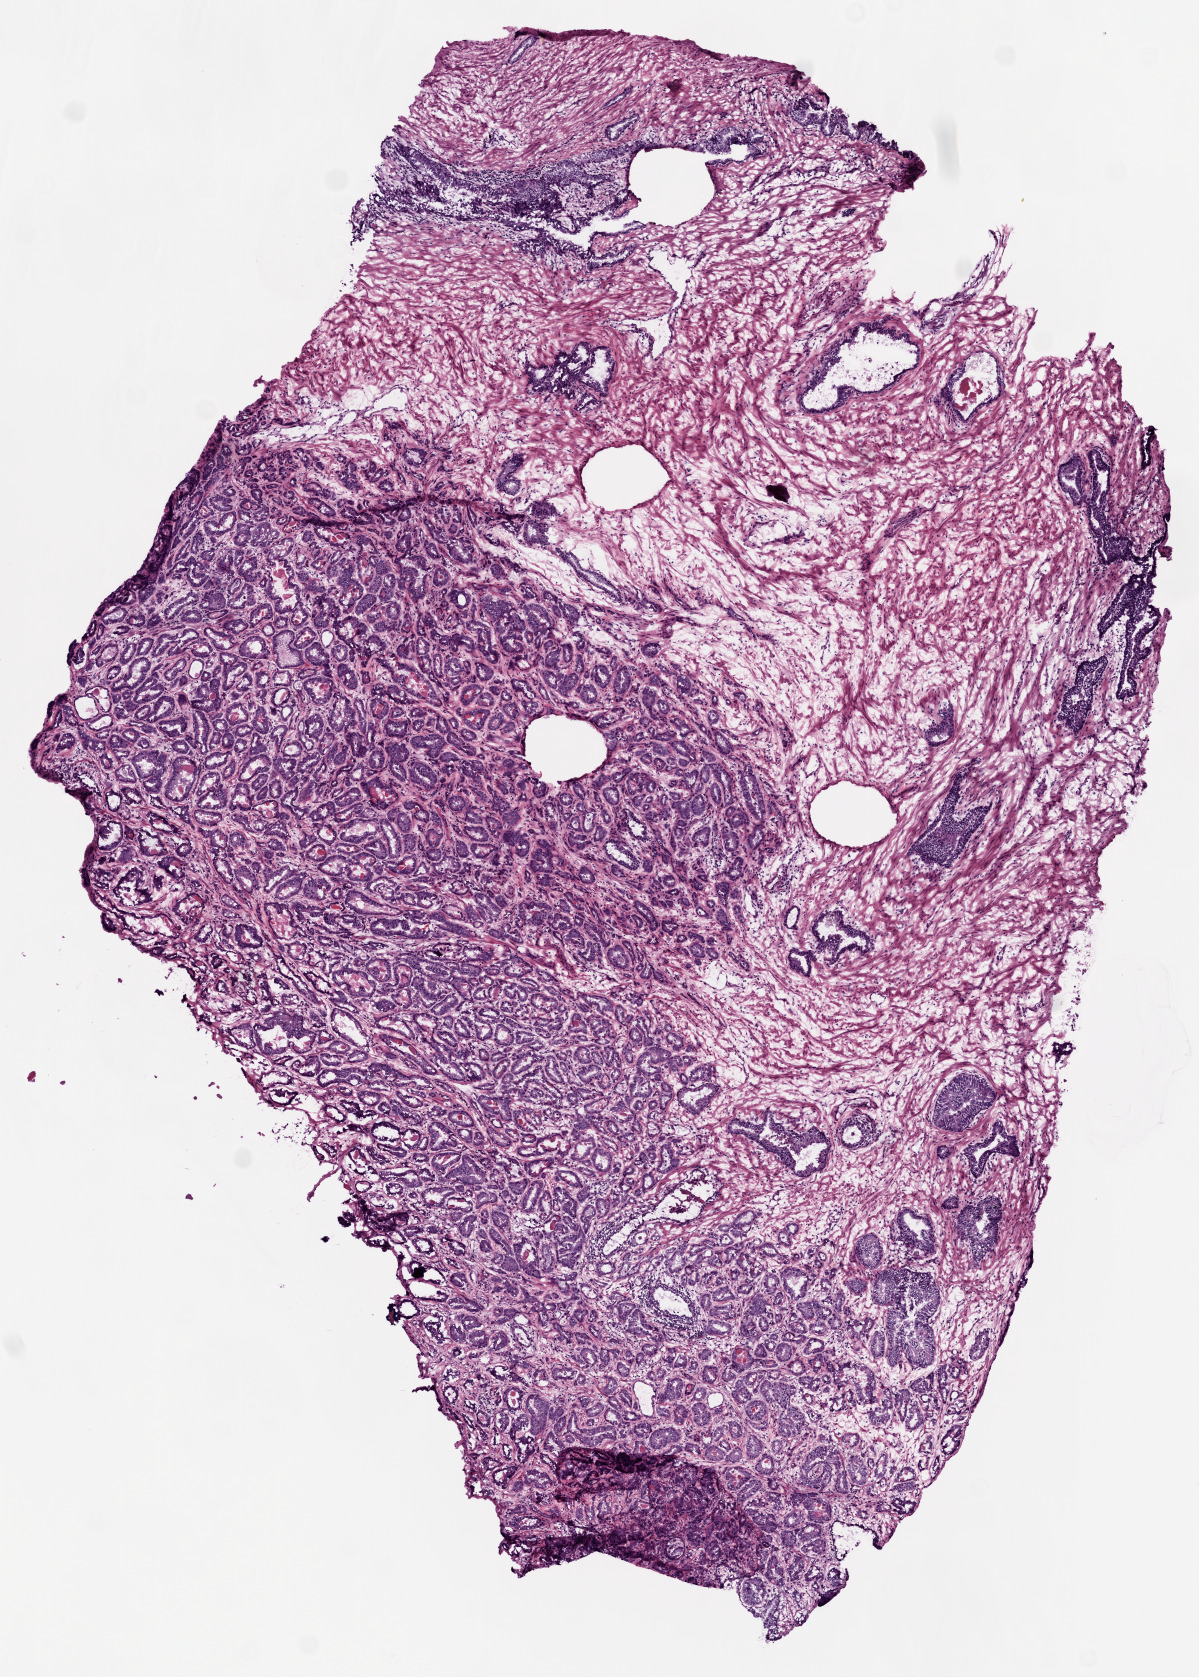
Whole-slide histology image, Hematoxylin and eosin (H&E) stained — low-resolution overview of the scanned area, about 4.8 x 6.8 mm (slide scanned at 20x). Frozen section from the top of the tissue portion. Sample: primary tumour, prostate. Male, age 56 years at initial diagnosis. Gleason score: 6 (3+3). Pathologist review of this section (percent, as recorded): tumour cells 90%, tumour nuclei 90%, normal cells 5%, stromal cells 5%, necrosis 0%.
Lymph nodes positive (case pathology): 0 of 2 examined. Pathologic diagnosis: Acinar cell carcinoma (prostate gland).